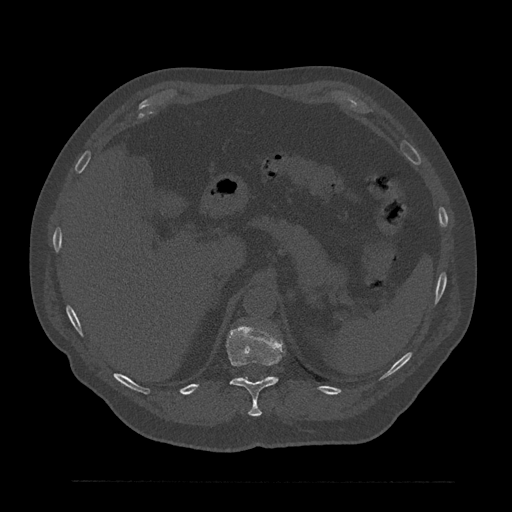
CT including the spine, one axial slice. Slice 280 of 797 in the series (ordered by position). Reconstruction kernel Br40s/3. 120 kVp. Bone window (W 1800 / L 400 HU). 0.5 mm slice thickness. 512 × 512 image matrix, field of view 430 × 430 mm. Male patient, age 61 years. Case-level facts recorded for this patient, not image findings: primary cancer: prostate.
Annotated regions visible in this slice (semi-automatic segmentation, software-assisted and operator-edited):
- T11 vertebra: bounding box (x1, y1, x2, y2) in pixels: (227, 325, 283, 416)